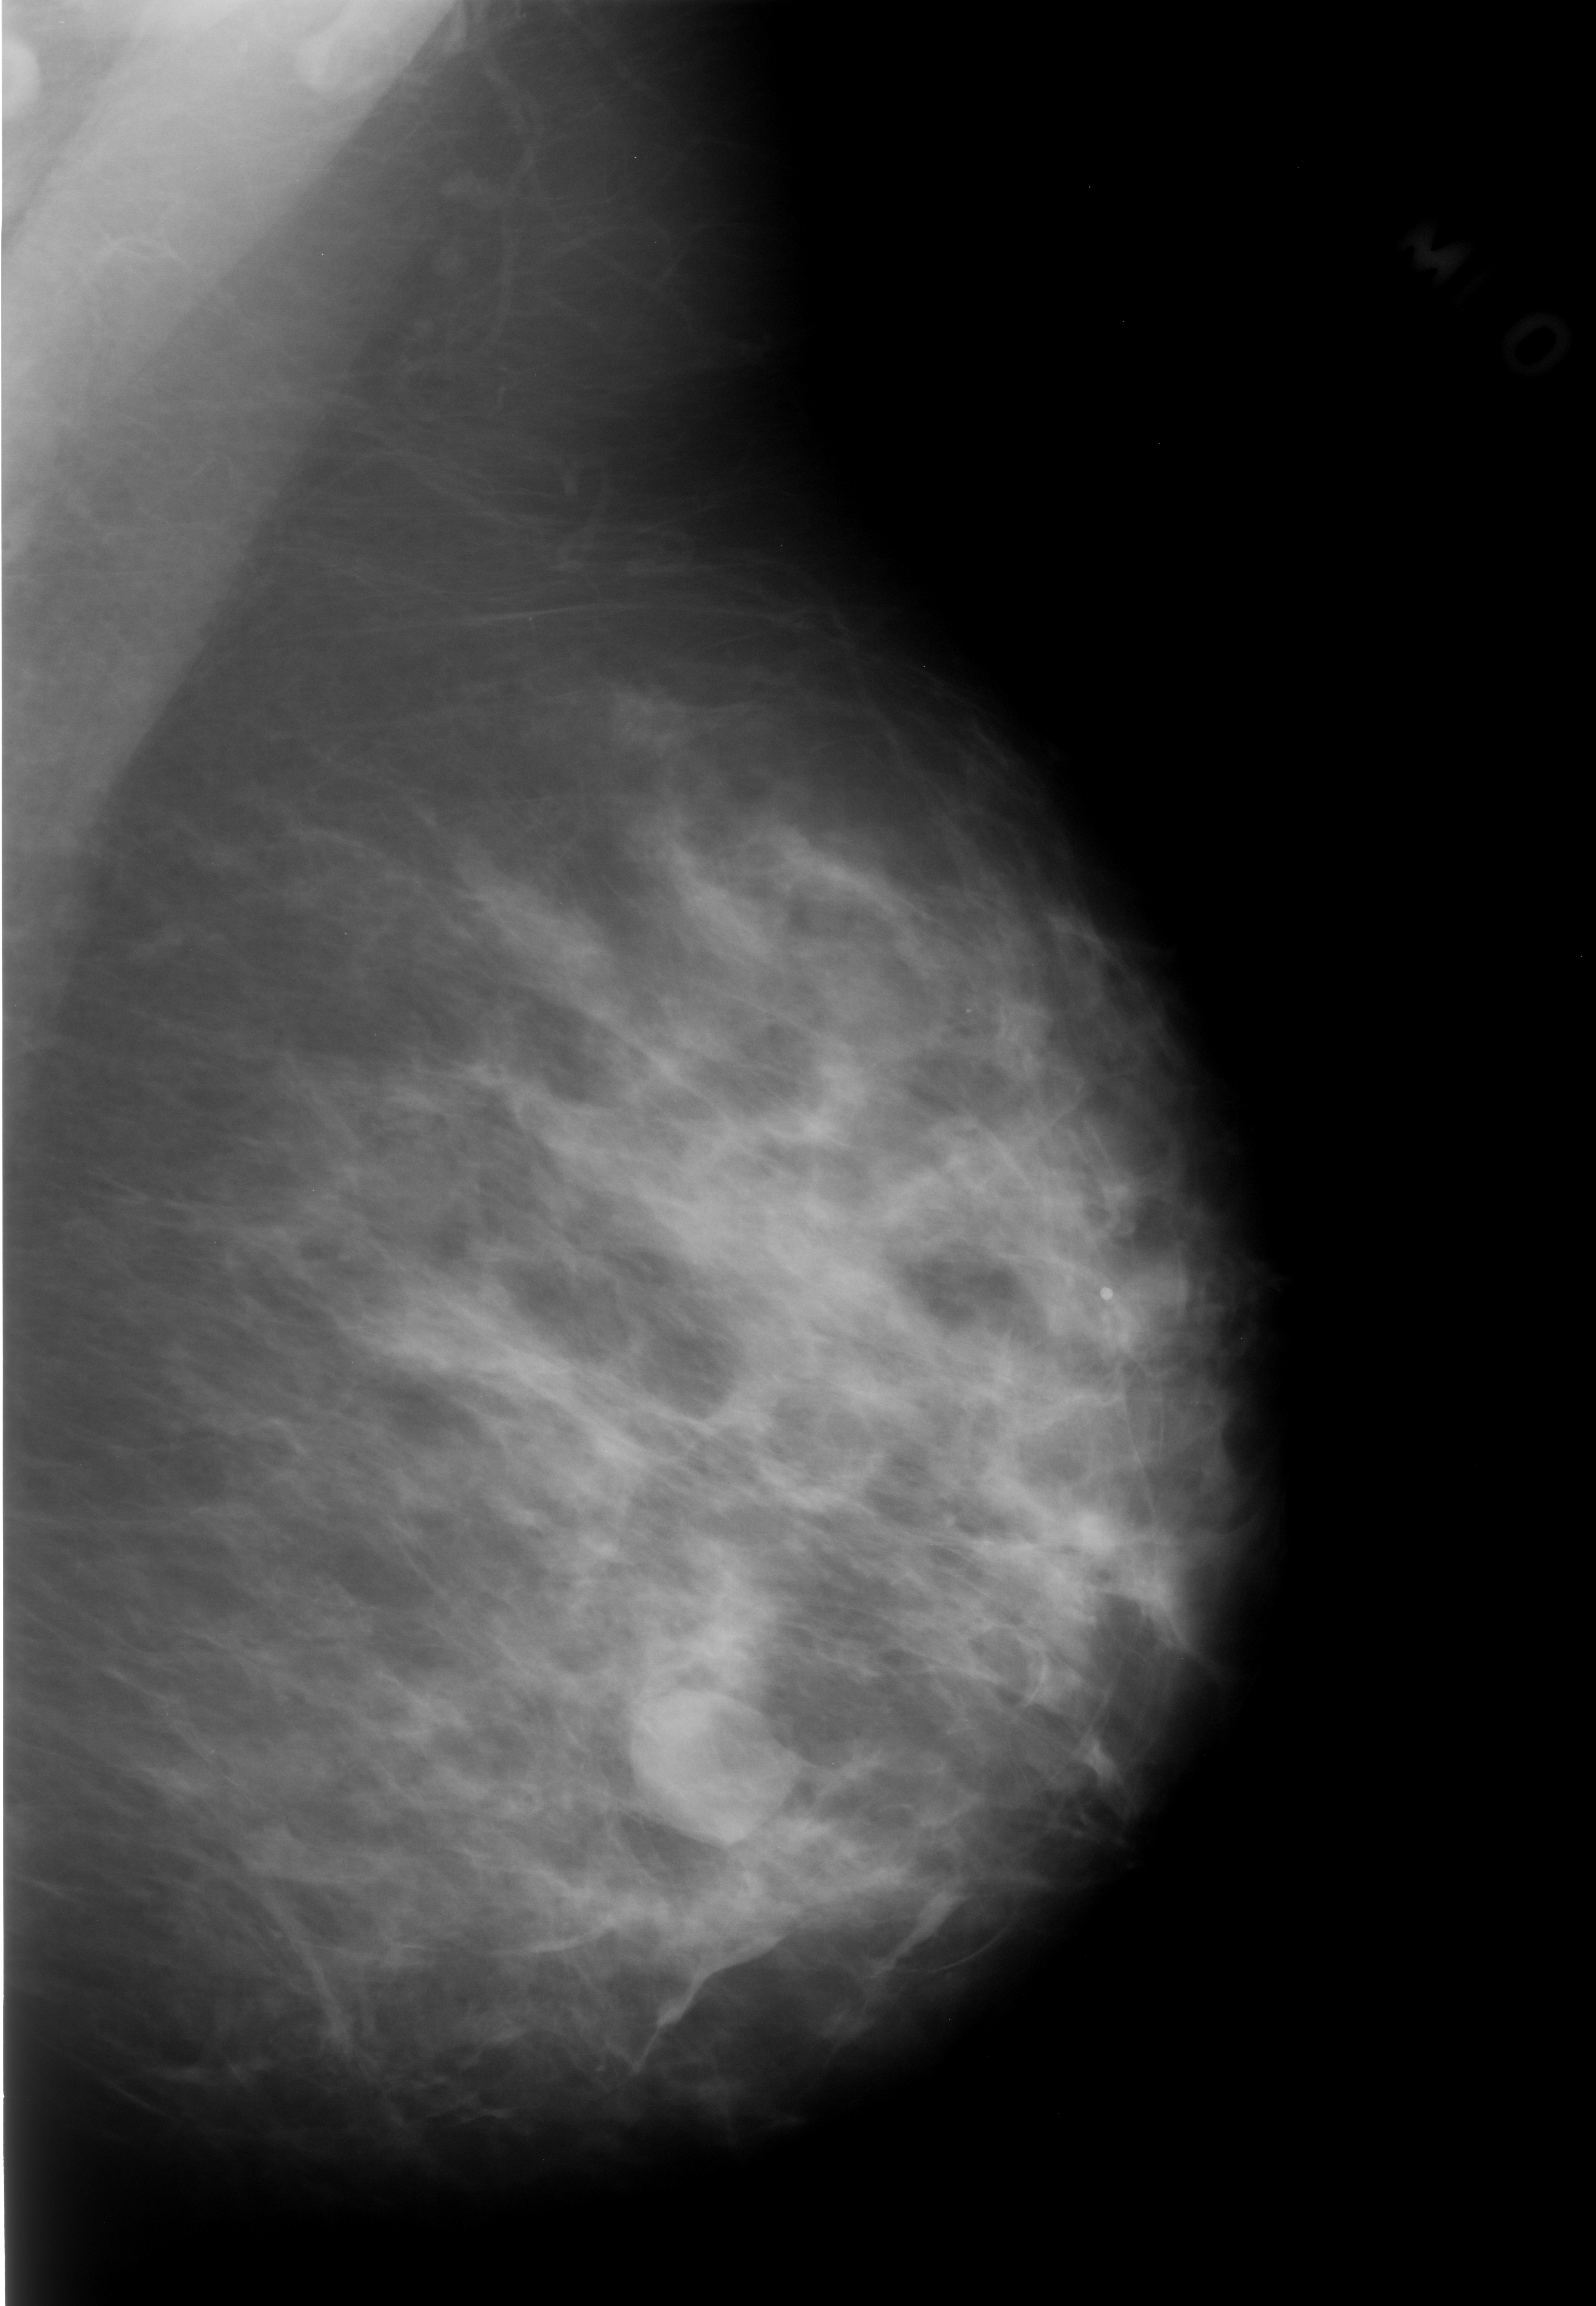
Digitized screen-film mammogram; left breast; MLO view; 1596 × 2306 image matrix.
Marked abnormalities (boxes around the expert regions of interest):
- mass, shape oval, margins circumscribed; BI-RADS assessment category 3; subtlety rating 5 on a 1 (subtle) to 5 (obvious) scale; pathology result (as recorded, not read from the image): benign: bounding box [x1, y1, x2, y2] px = [624, 1693, 795, 1848]